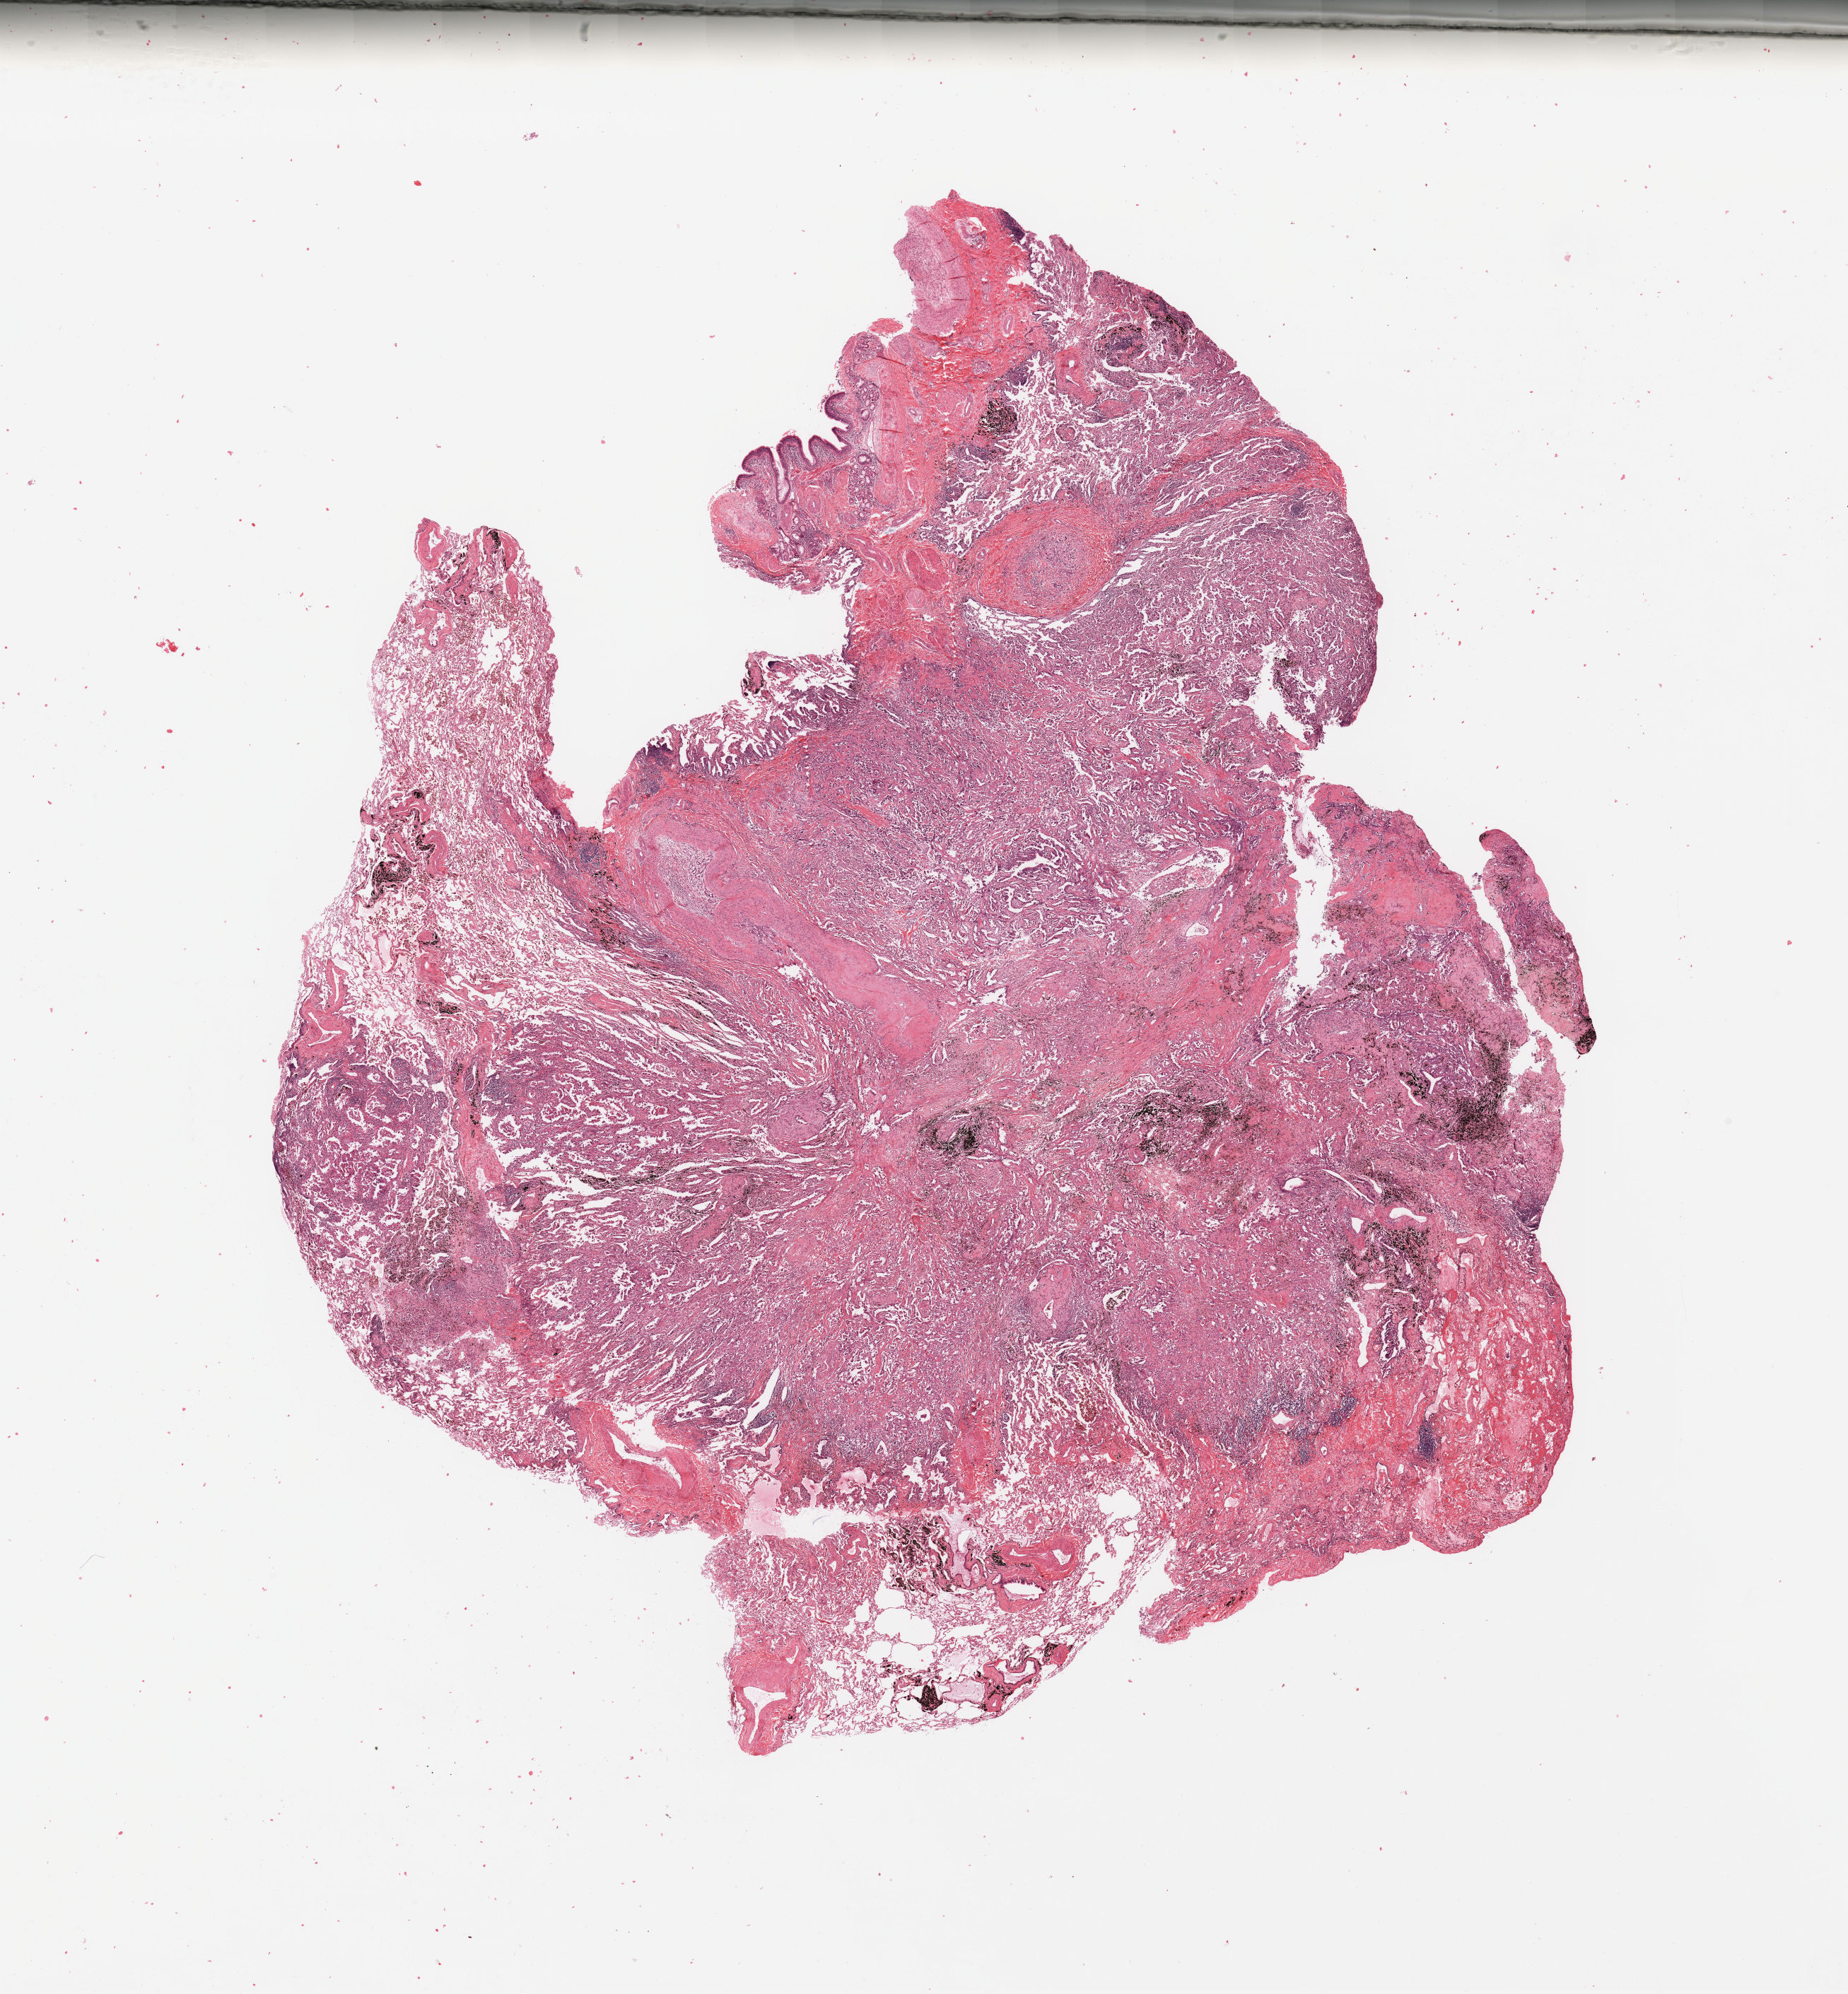
Hematoxylin and eosin (H&E) stained whole-slide image — a low-resolution overview of the entire scanned area, about 20.7 x 22.3 mm (slide scanned at 20x), tumour tissue sample, lung. Patient: male, age 59 years. Histologic grade: G2 (moderately differentiated).
Primary tumour site (as recorded): right upper lobe. Histologic diagnosis: Adenocarcinoma, NOS. AJCC pathologic stage: IIIA.